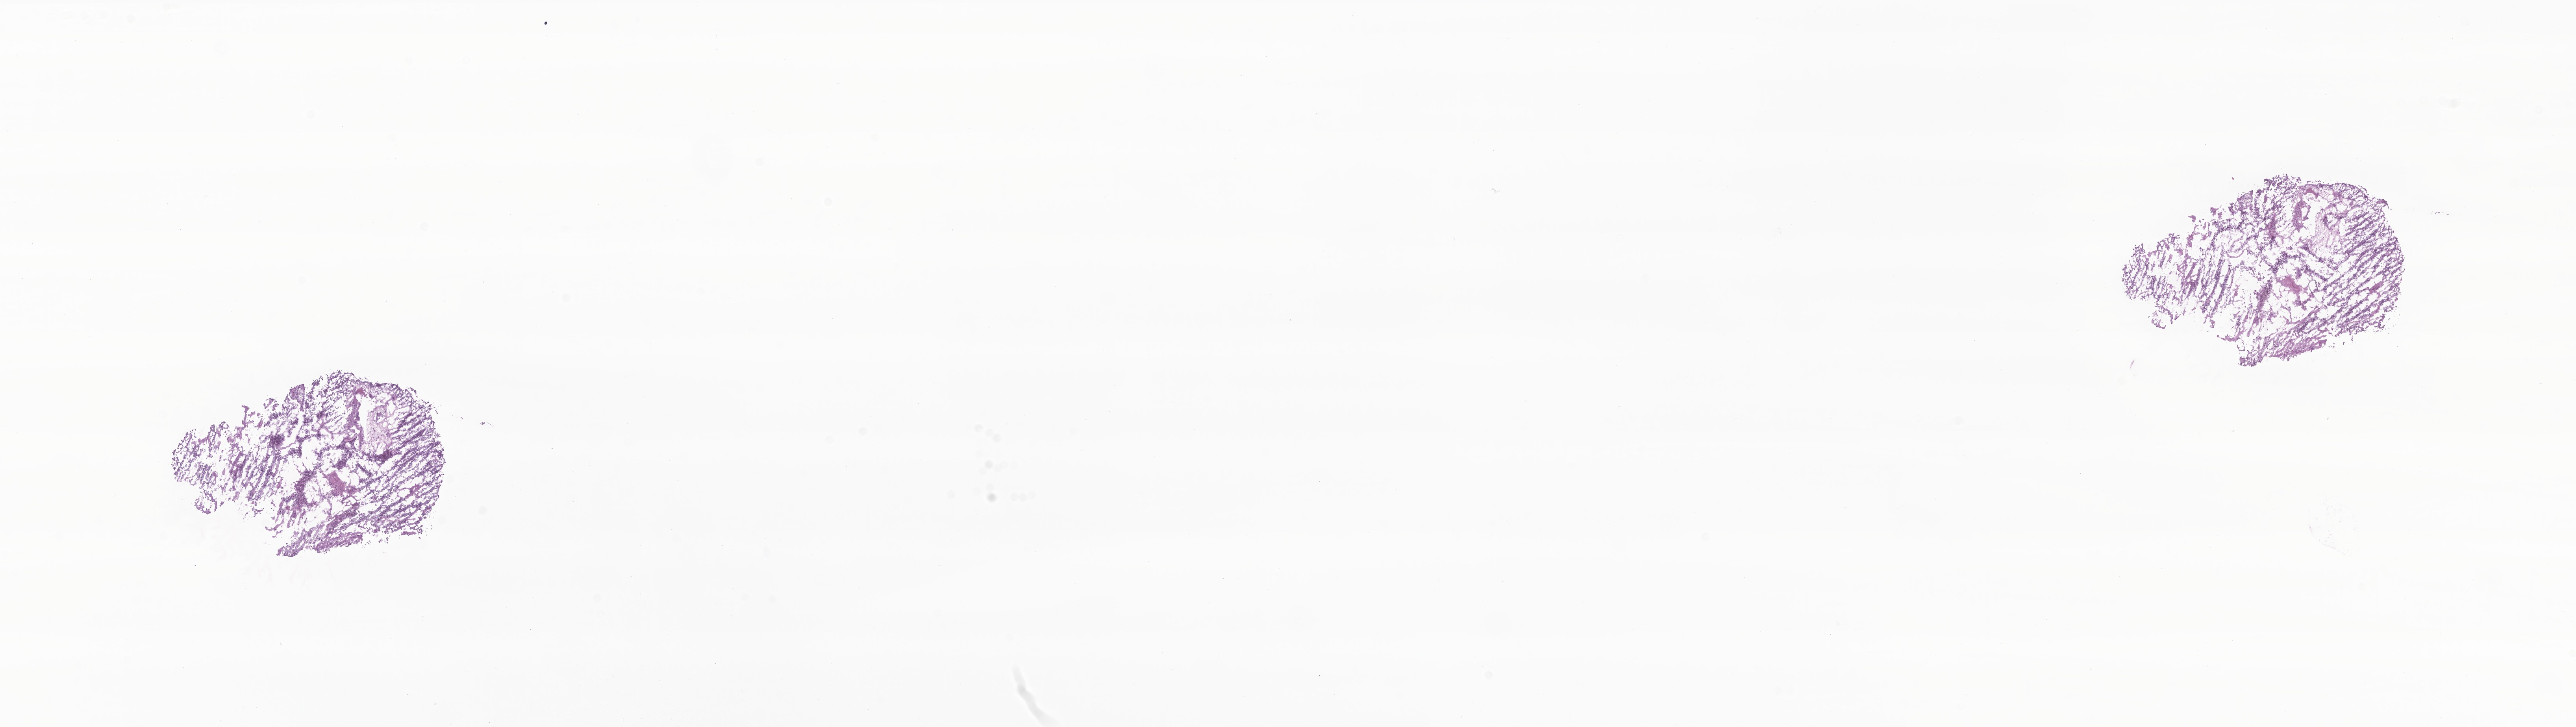
Whole-slide image, haematoxylin and eosin stain of tumor tissue from the frontal lobe, shown as a low-resolution overview of the whole scanned area (about 27.6 x 7.8 mm). Frozen section (OCT-embedded). Patient: male, age 205 months (17 years 1 month).
- diagnosis: Glioblastoma, NOS